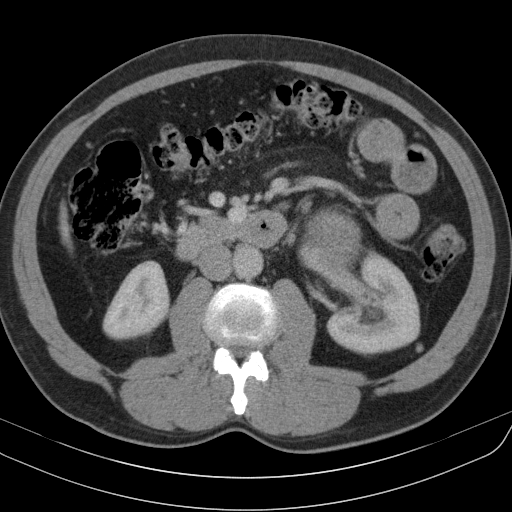
Contrast-enhanced abdominal CT, one axial slice; position 54 of 91 along the scan axis; reconstruction kernel B31s; 130 kVp; intravenous contrast given; soft-tissue window (W 400 / L 40 HU); 5 mm slice thickness; 512 × 512 image matrix, field of view 370 × 370 mm. Male patient, age 51 years. From the clinical record (not read from this slice): diagnosis: adrenocortical carcinoma; tumour side: left adrenal; tumour size at pathology: 18 cm; Ki-67 index: 40 %; stage (as recorded): 3.
Annotated regions visible in this slice (semi-automatically segmented with operator editing):
- mass: bounding box (x1, y1, x2, y2) in pixels: (309, 211, 360, 270)